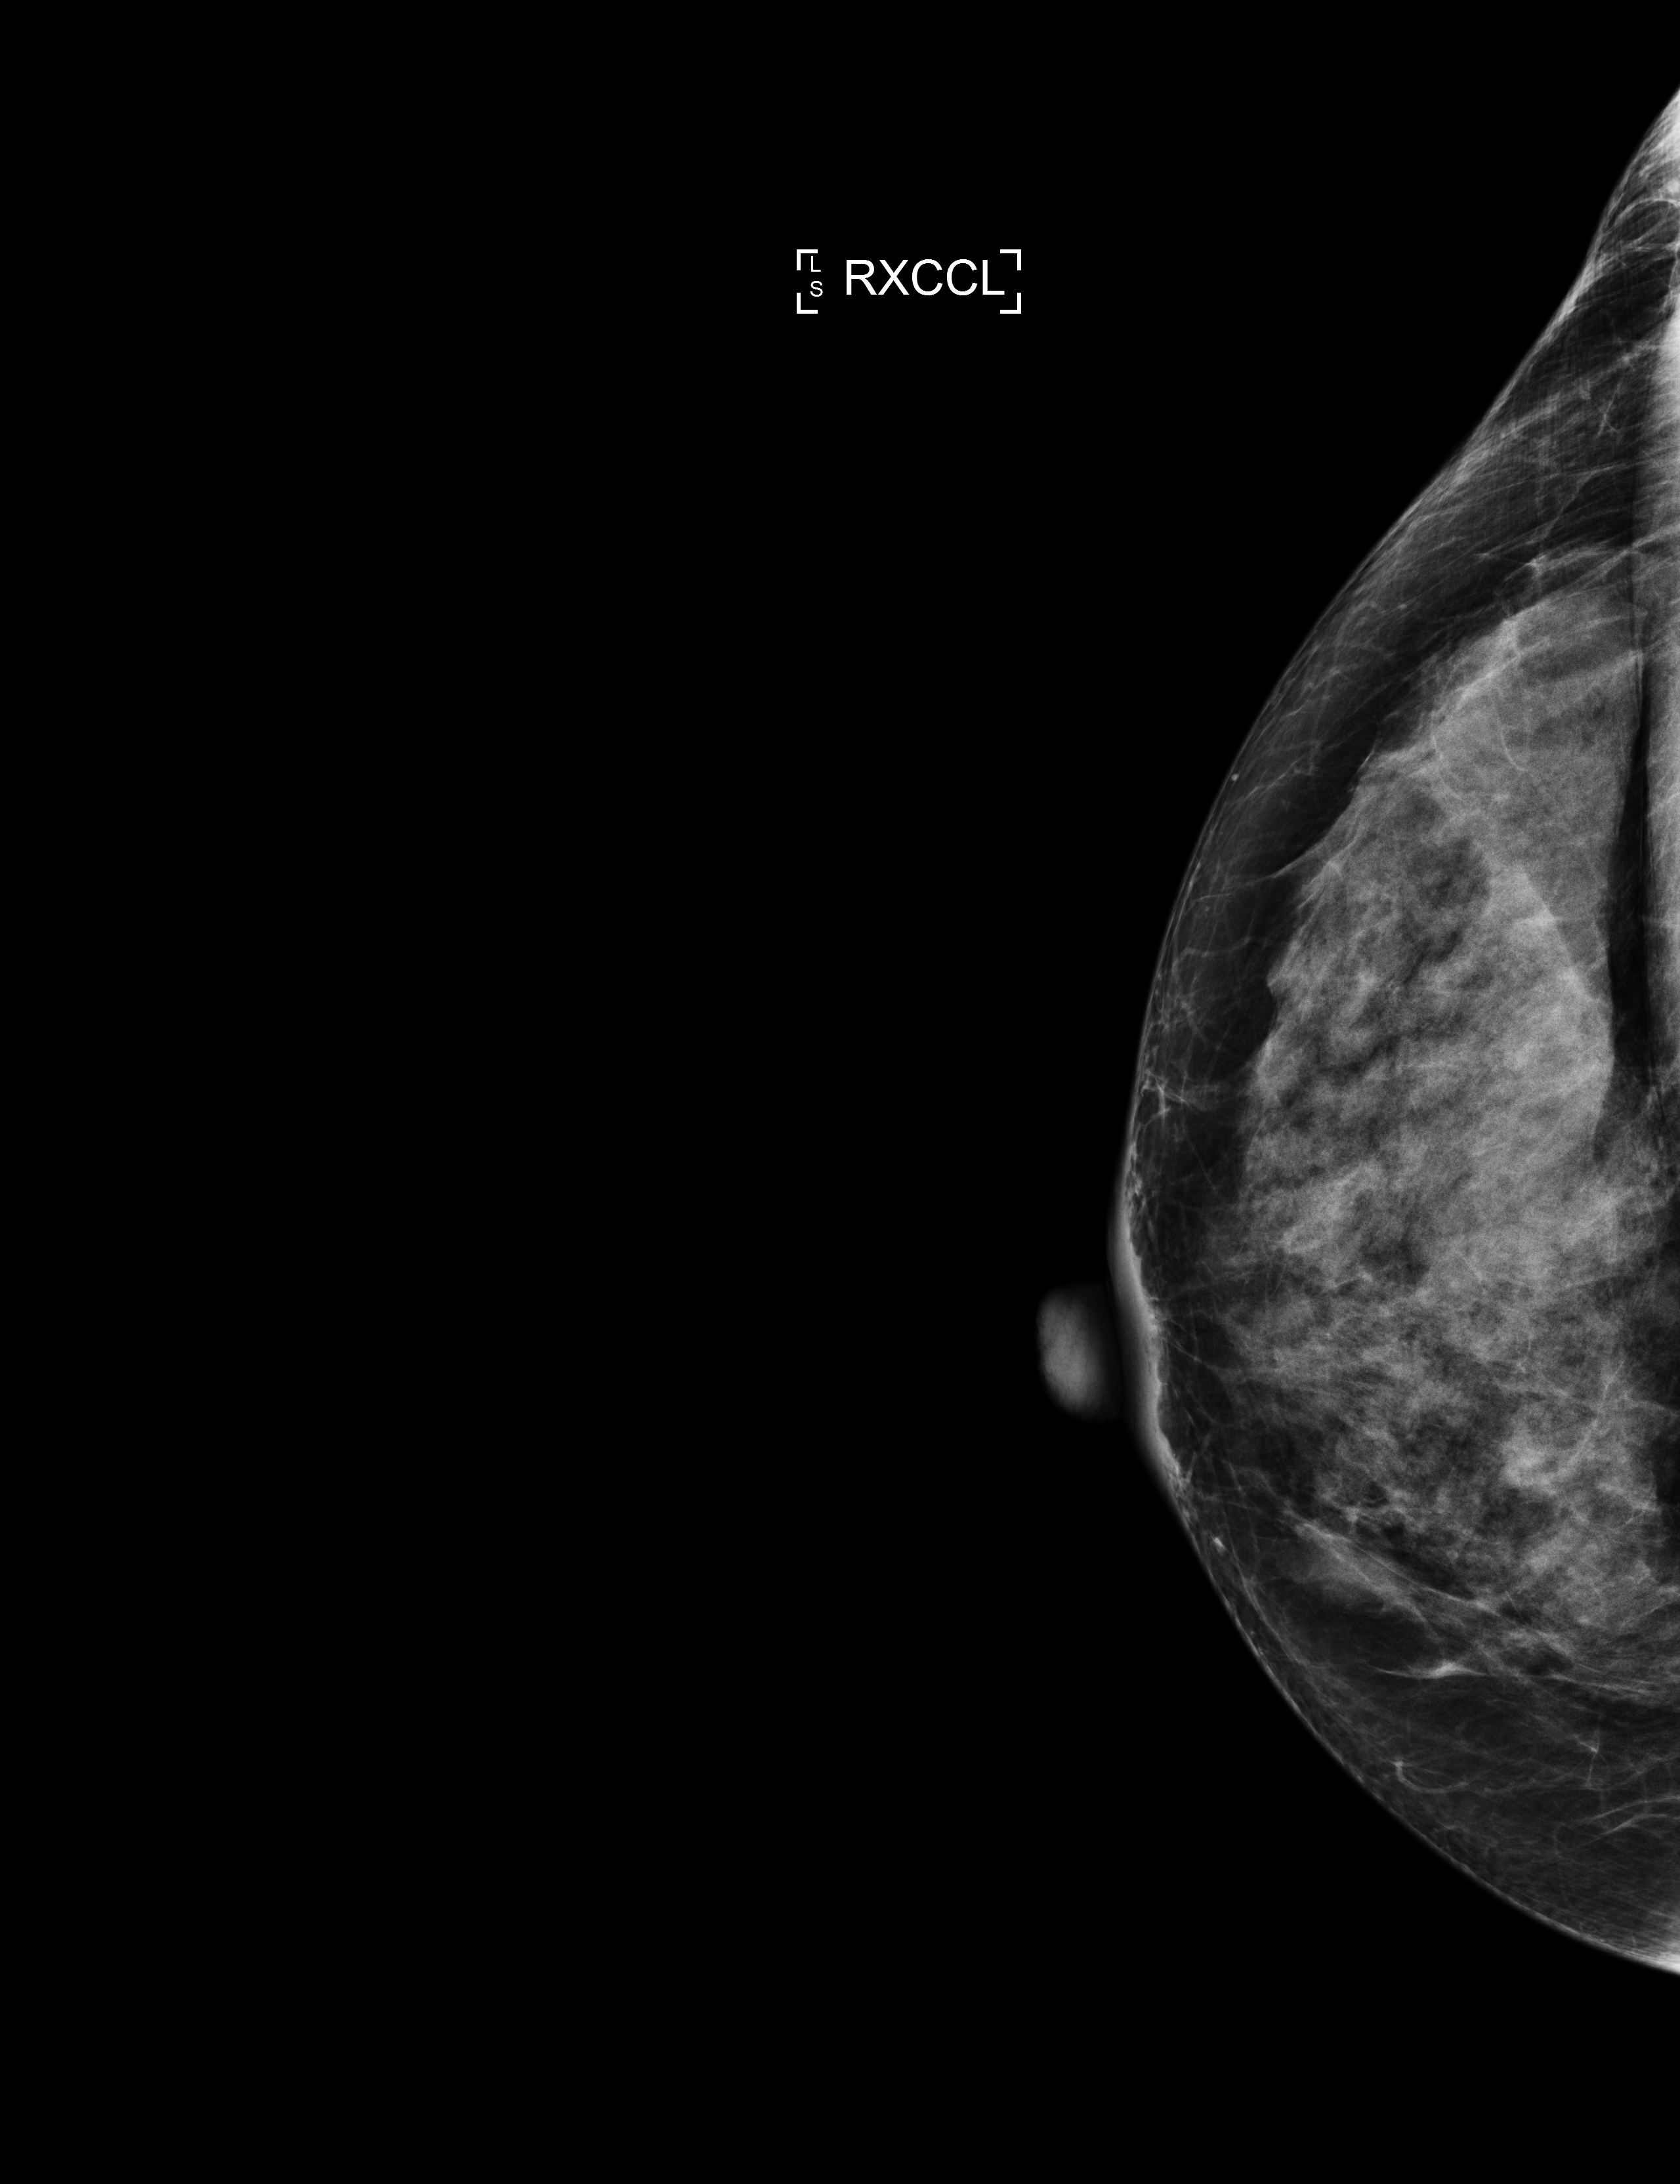
Full-field digital mammogram (FFDM), right breast, exaggerated CC view (lateral), annual screening mammography examination. Patient aged 67 years (female).
BI-RADS breast density category at the screening exam (both breasts, scale 1–4): 4. Final BI-RADS category for the screening round (tomosynthesis exam, both breasts): category 2. Recall: no recall after this screen.